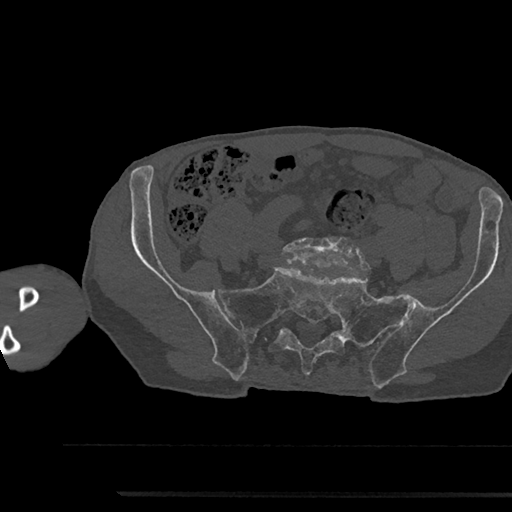
CT including the spine, one axial slice; slice 292 of 797 in the series (ordered by position); reconstruction kernel Br40s/3; 120 kVp; bone window (W 1800 / L 400 HU); 0.5 mm slice thickness; 512 × 512 image matrix, field of view 367 × 367 mm. Male patient, age 79 years. From the clinical record (not read from this slice): primary cancer: prostate.
Annotated regions visible in this slice (semi-automatically segmented with operator editing):
- L5 vertebra: bounding box (x1, y1, x2, y2) in pixels: (282, 237, 361, 268)